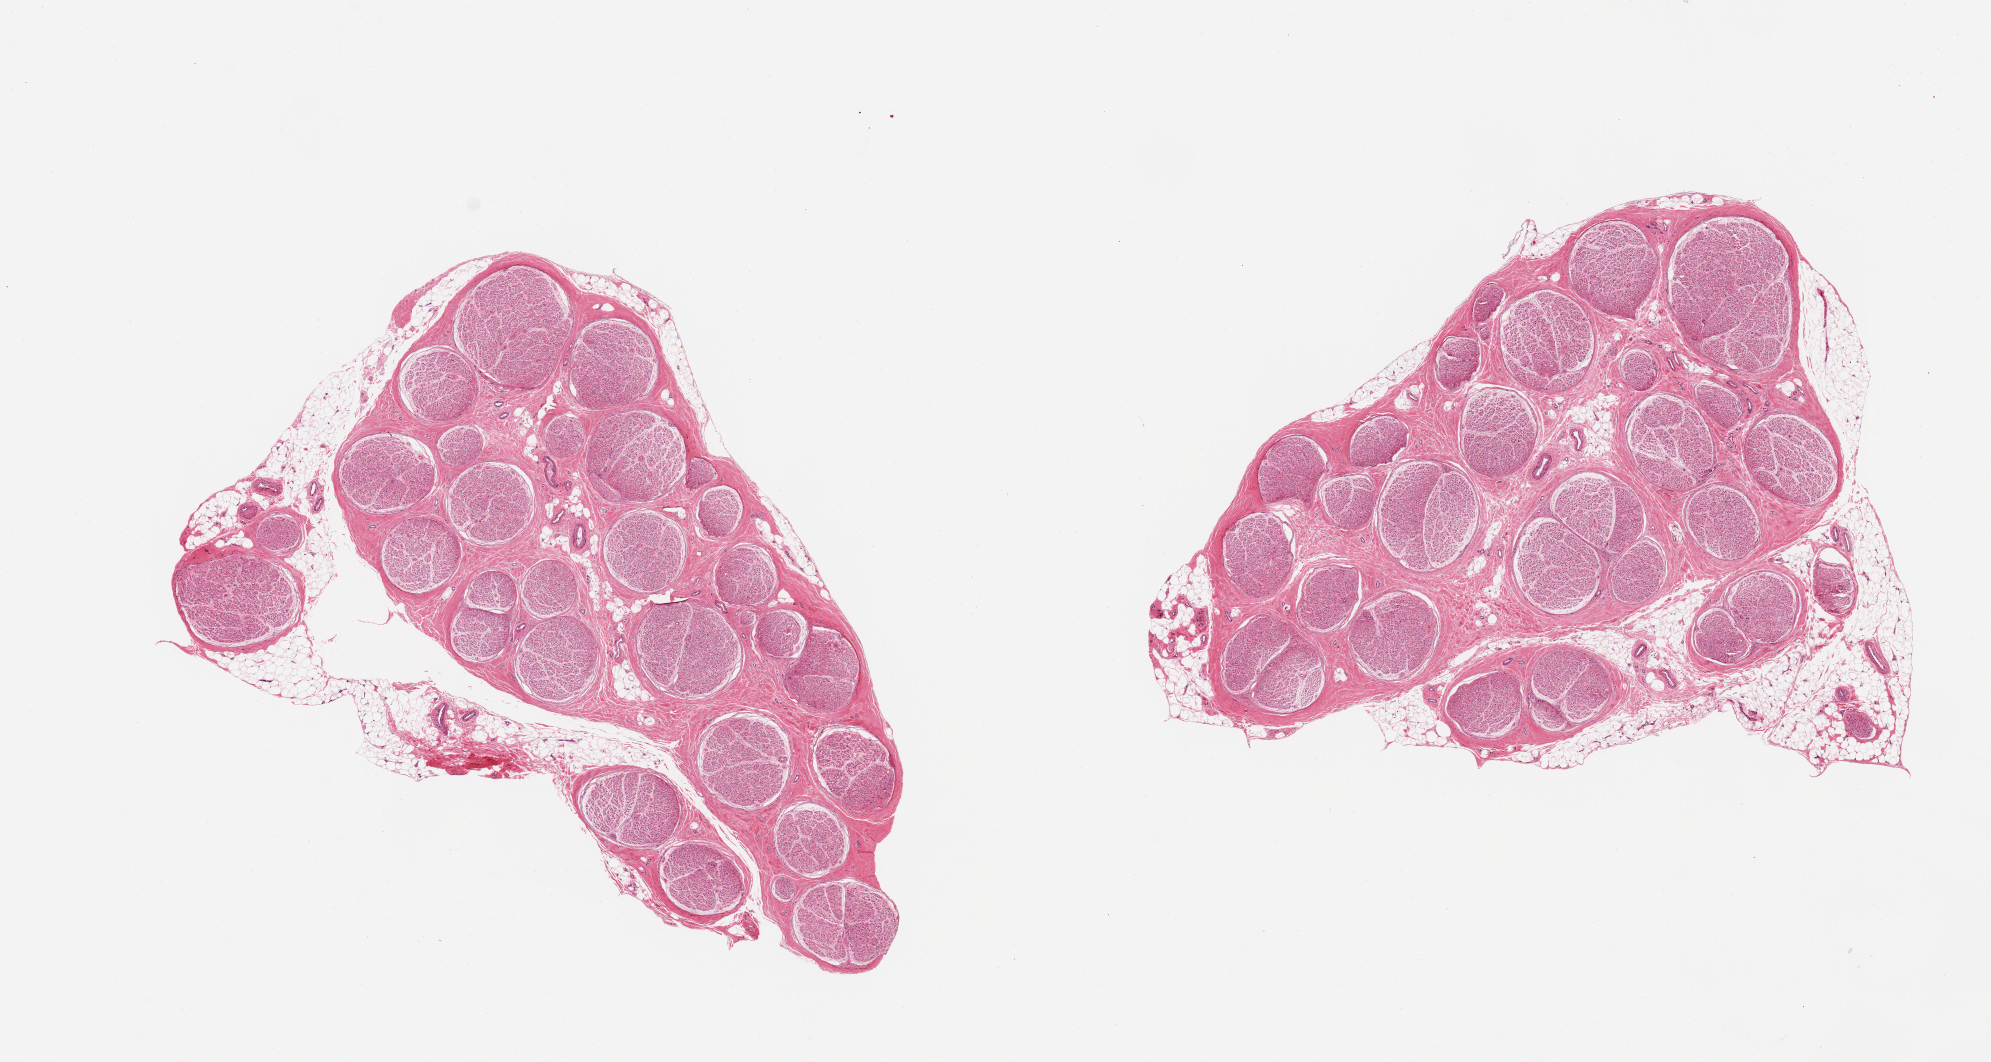
Digitized hematoxylin and eosin (H&E)-stained section — low-resolution overview of the scanned area, about 15.8 x 8.4 mm. PAXgene-fixed, paraffin-embedded tissue. Sampled site (target tissue): tibial nerve. Tissue donor sample.
* review note (as recorded): 2 ~6x5mm aliquots, ~10% interstitial/peripheral adipose tissue